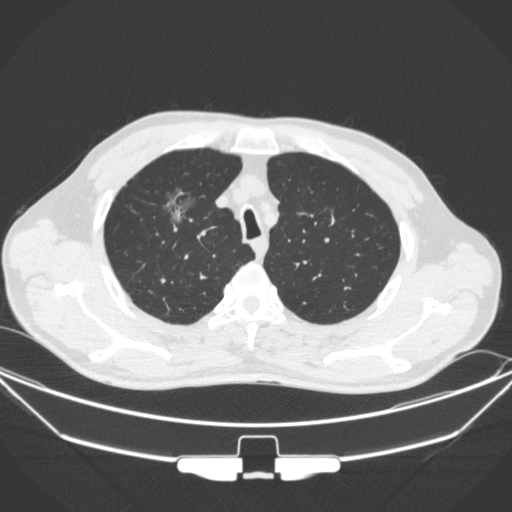
Chest CT, one axial slice. Position 278 of 355 along the scan axis. 120 kVp. Lung window (W 1500 / L -600 HU). 512 × 512 image matrix, field of view 399 × 399 mm. Male patient, age 67 years. Case-level facts recorded for this patient, not image findings: clinical TNM (as recorded): T1c N0 M0.
Annotated regions visible in this slice (bounding box drawn by a radiologist):
- lung tumour (recorded histology: adenocarcinoma): box from (x=162, y=179) to (x=205, y=231) px